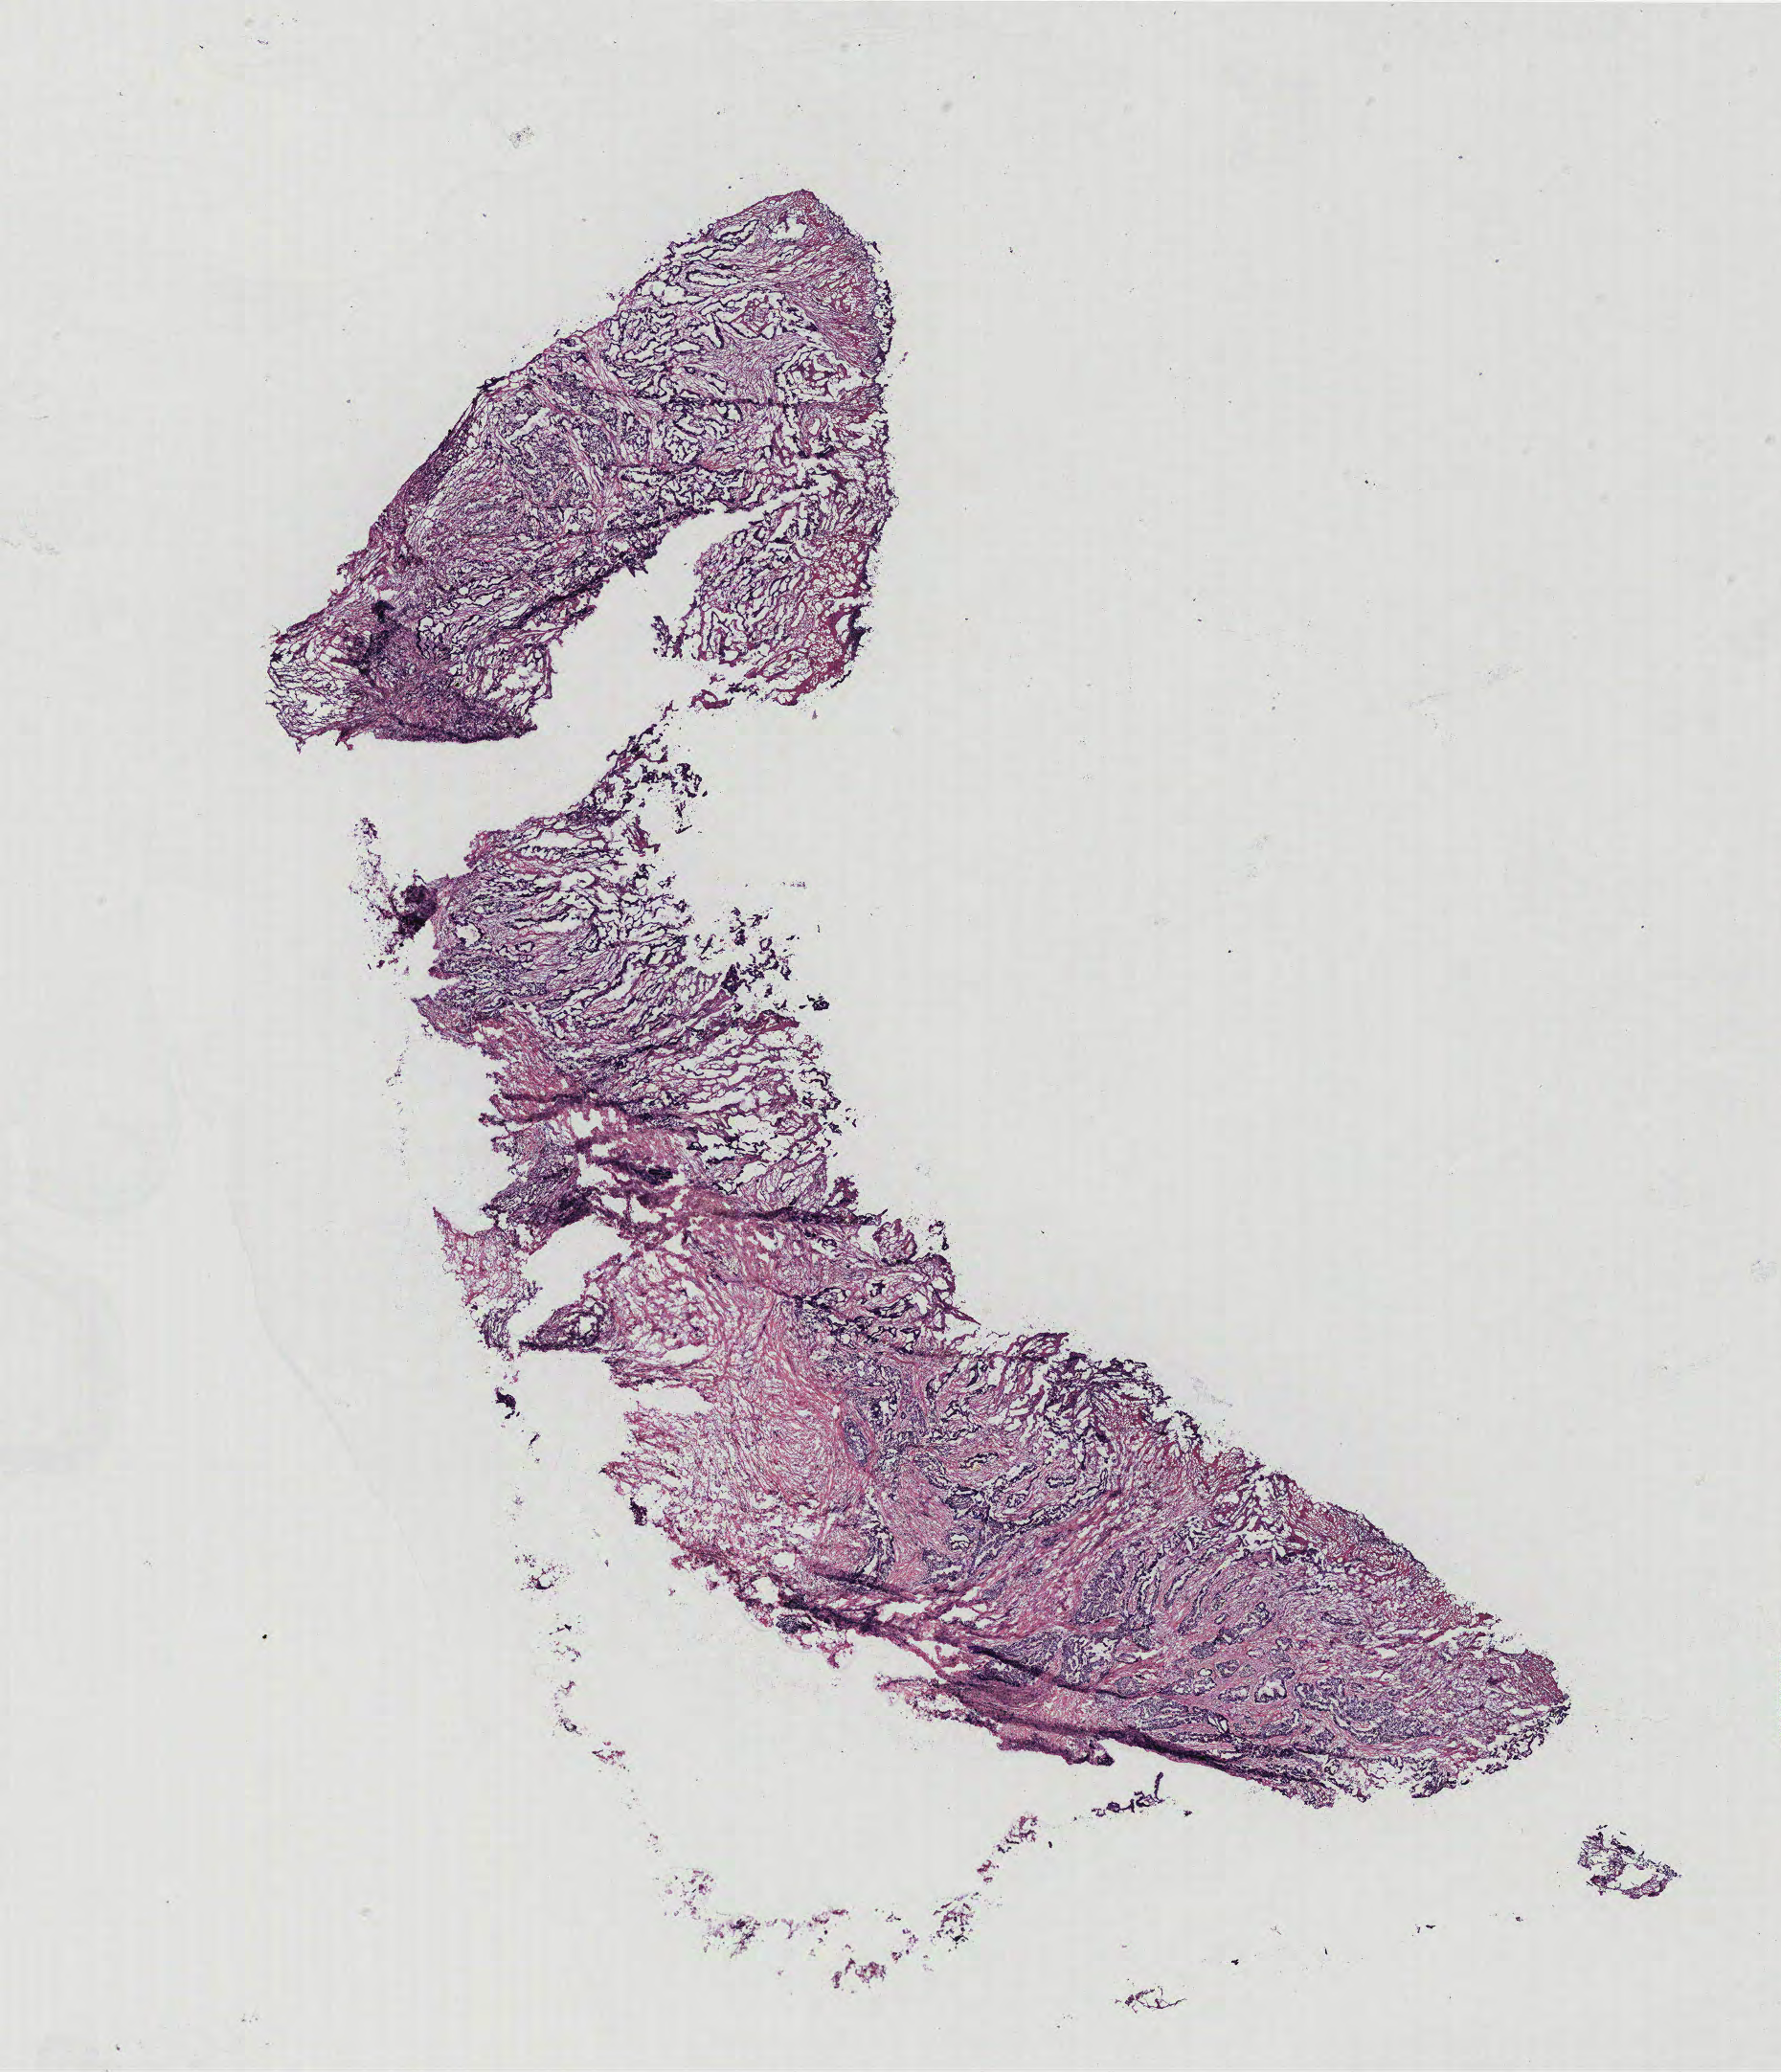
Whole-slide histology image, H&E-stained, shown as a low-resolution overview of the whole scanned area (about 14.9 x 17.3 mm, from a 40x scan), colon, normal (non-tumour) tissue. Patient: female, age 54 years.
This section: normal (non-tumour) tissue from the same patient. Patient diagnosis: Adenocarcinoma, NOS.